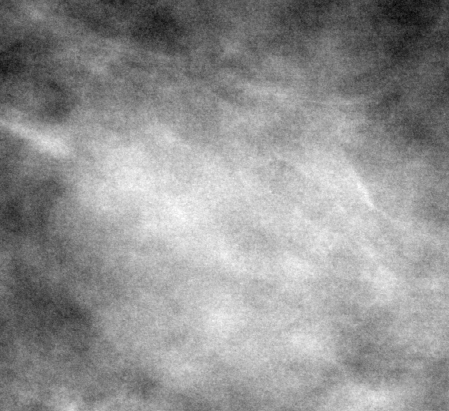
Crop from a digitized film mammogram around one marked abnormality; right breast; MLO view.
Marked abnormality: mass, shape oval, margins circumscribed; BI-RADS assessment category 4; pathology result (as recorded, not read from the image): benign.